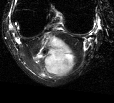
MRI of an extremity soft-tissue mass, one axial slice; slice 13 of 44 in the series (ordered by position); T2-weighted fat-saturated; MR volume resampled by the dataset authors to the PET/CT grid (not the native acquisition matrix); 3.27 mm slice thickness; 114 × 103 image matrix, field of view 111 × 101 mm. Female patient. Case-level facts recorded for this patient, not image findings: histological type: liposarcoma; site of the primary tumour: right thigh.
Outlined on this slice (expert contour drawn on MRI and transferred to this co-registered scan by the dataset authors):
- gross tumour volume (mass): box from (x=33, y=33) to (x=76, y=76) px